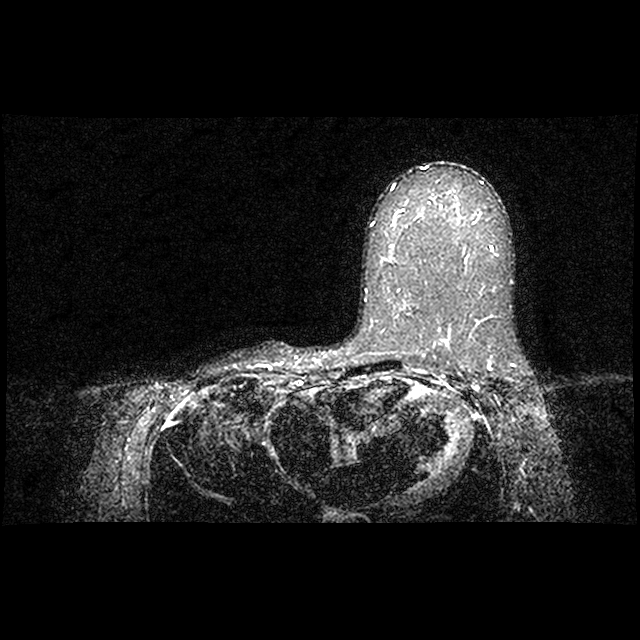
Breast MRI examination; 1 image, one mid-volume slice chosen by position.
Image 1: fluid-sensitive (T2/STIR) axial slice, series "STIR SENSE", slice 46 of 90.
Patient-level pathology facts (from the clinical record, not from the images): pathology diagnosis: invasive ductal CA (right breast); receptor status (as recorded): ER pos, PR pos, HER2 neg; Ki-67 (as recorded): high prolif; pathology report notes: mastectomy [date] show invasive ductal with axillary mets.